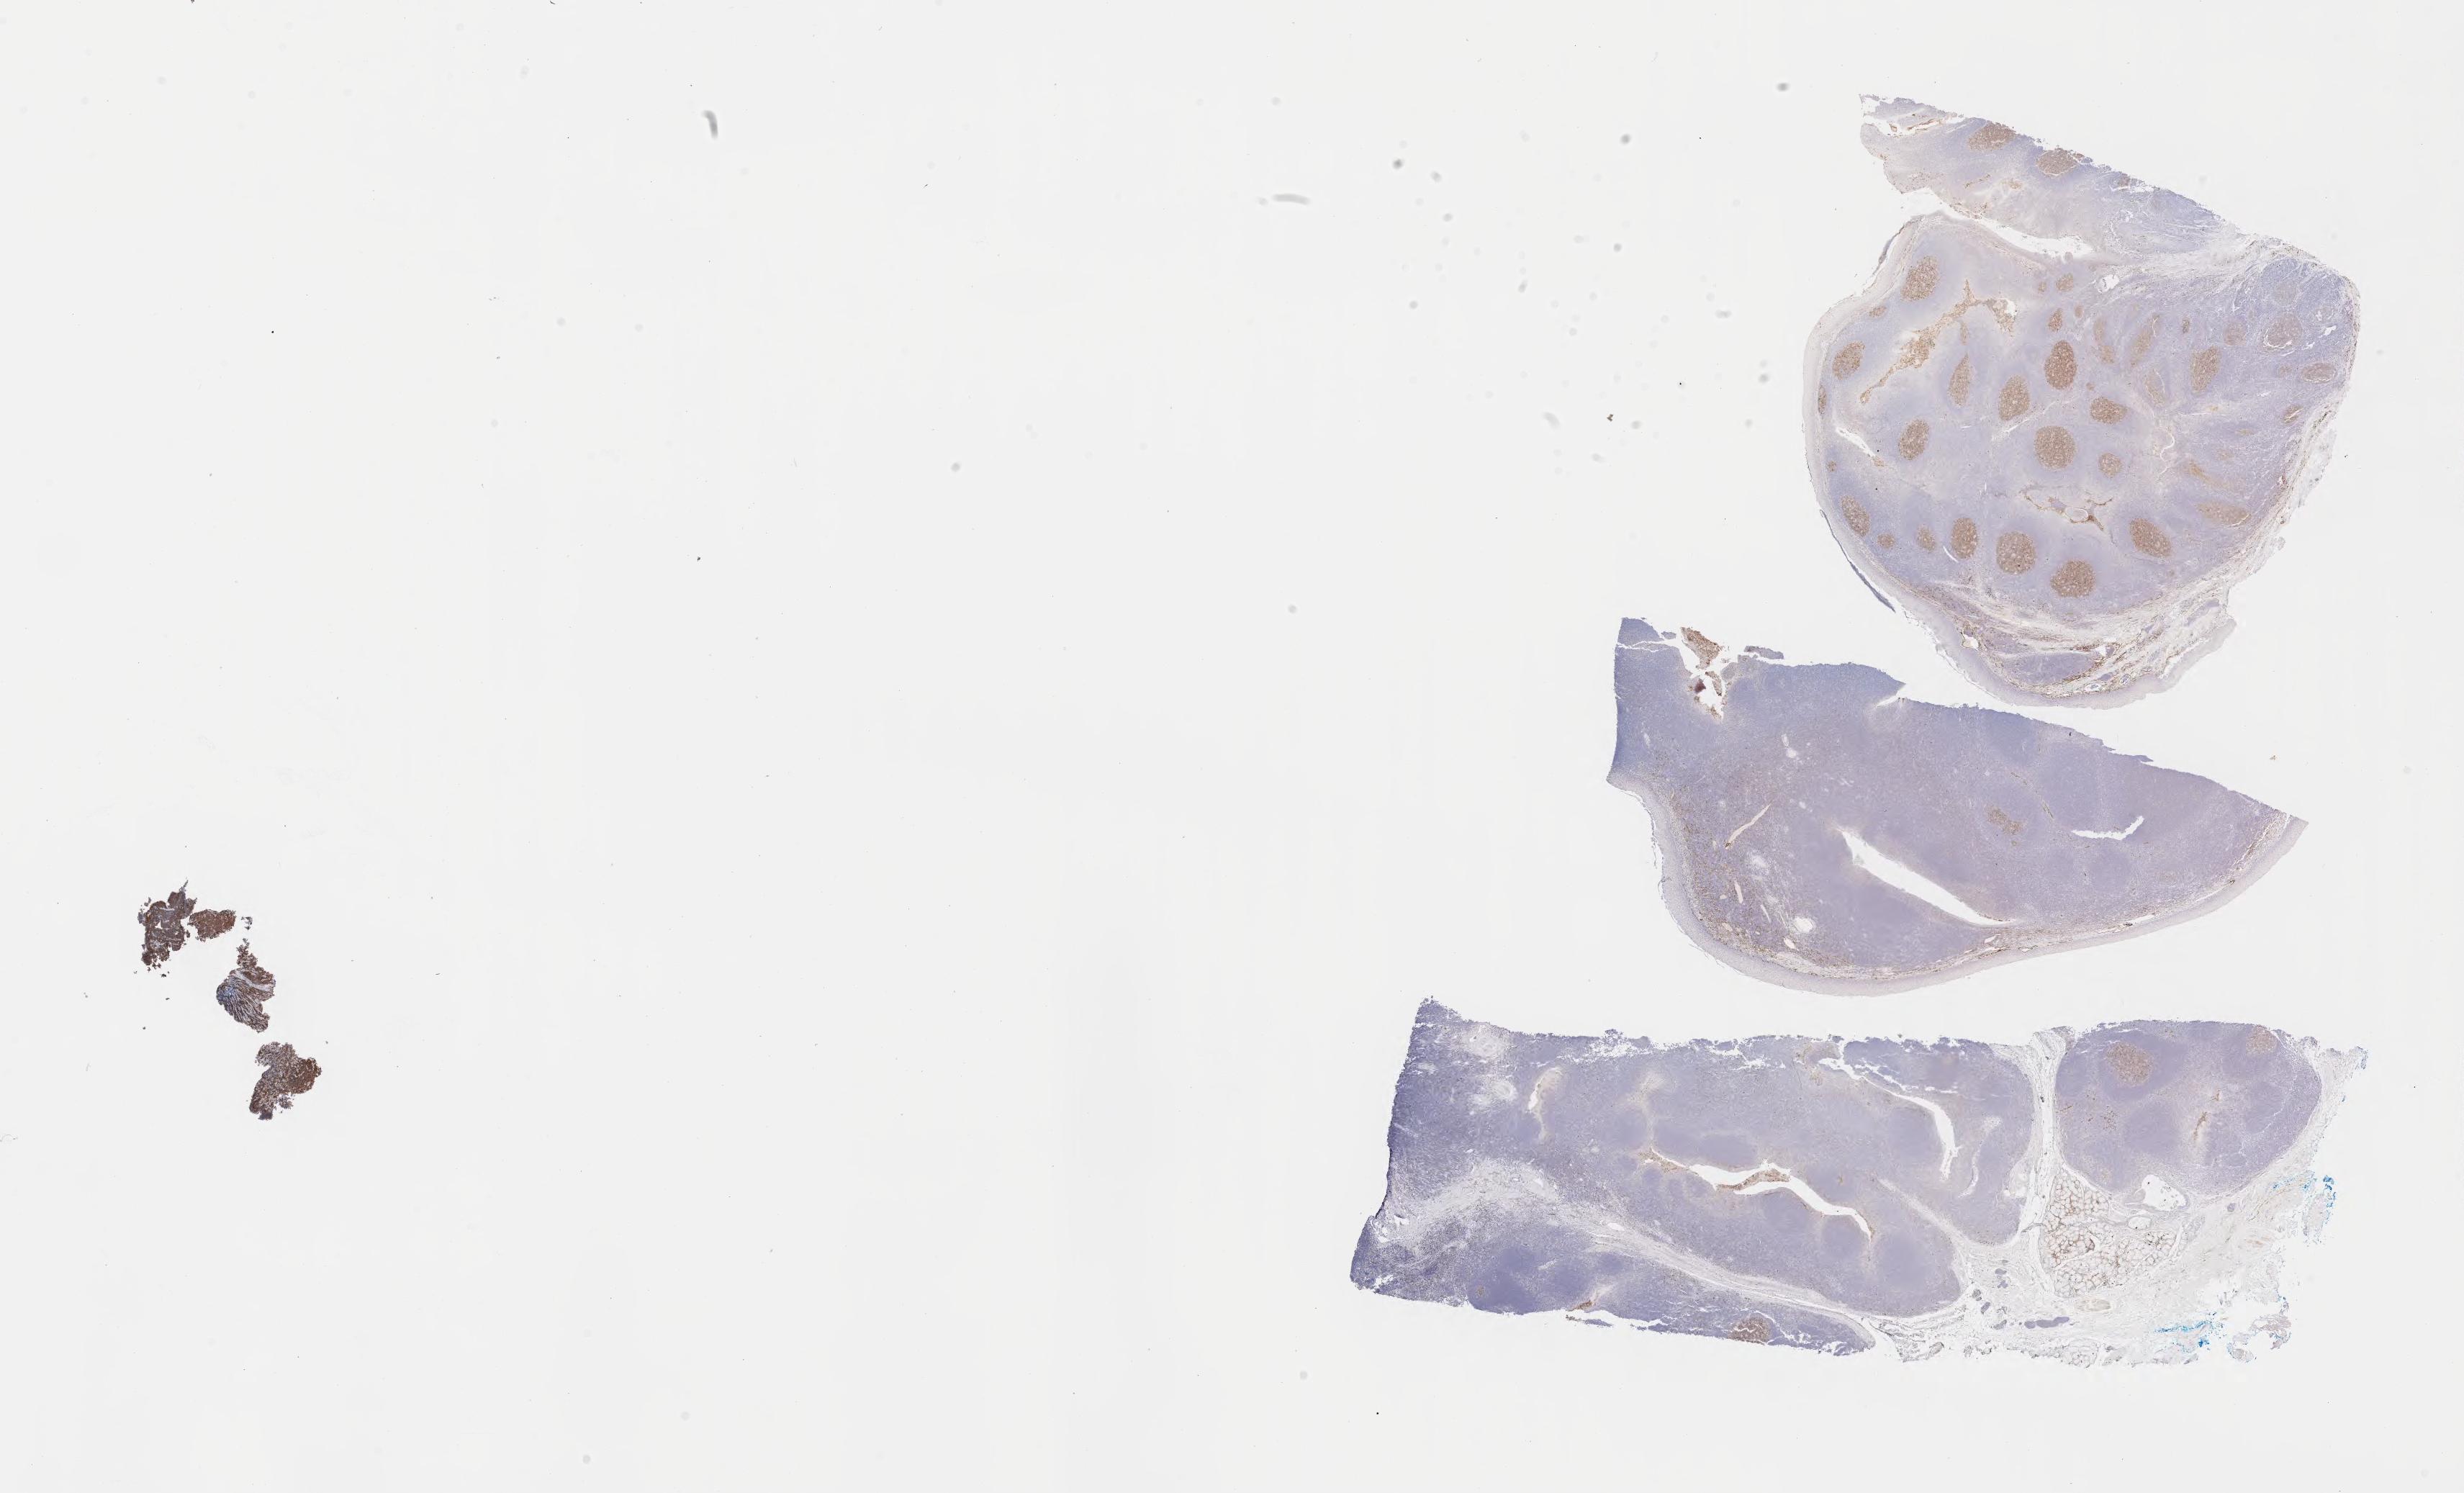
Whole-slide image, immunohistochemical stain for CD10 — low-resolution overview of the scanned area, about 27.7 x 16.8 mm. Tumor tissue. Site: abdomen proper. Male patient; age at initial diagnosis 6 years.
* diagnosis: Burkitt lymphoma, NOS